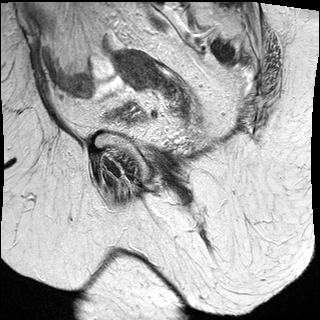
Pelvic MRI for cervical cancer, one sagittal slice; position 10 of 27 along the scan axis; T2-weighted; 1.5 T; TE 89 ms, TR 2740 ms; 320 × 320 image matrix. Female patient, age 67 years.
Annotated regions visible in this slice (outlined manually by an expert reader):
- uterus and cervix: box from (x=112, y=48) to (x=178, y=93) px